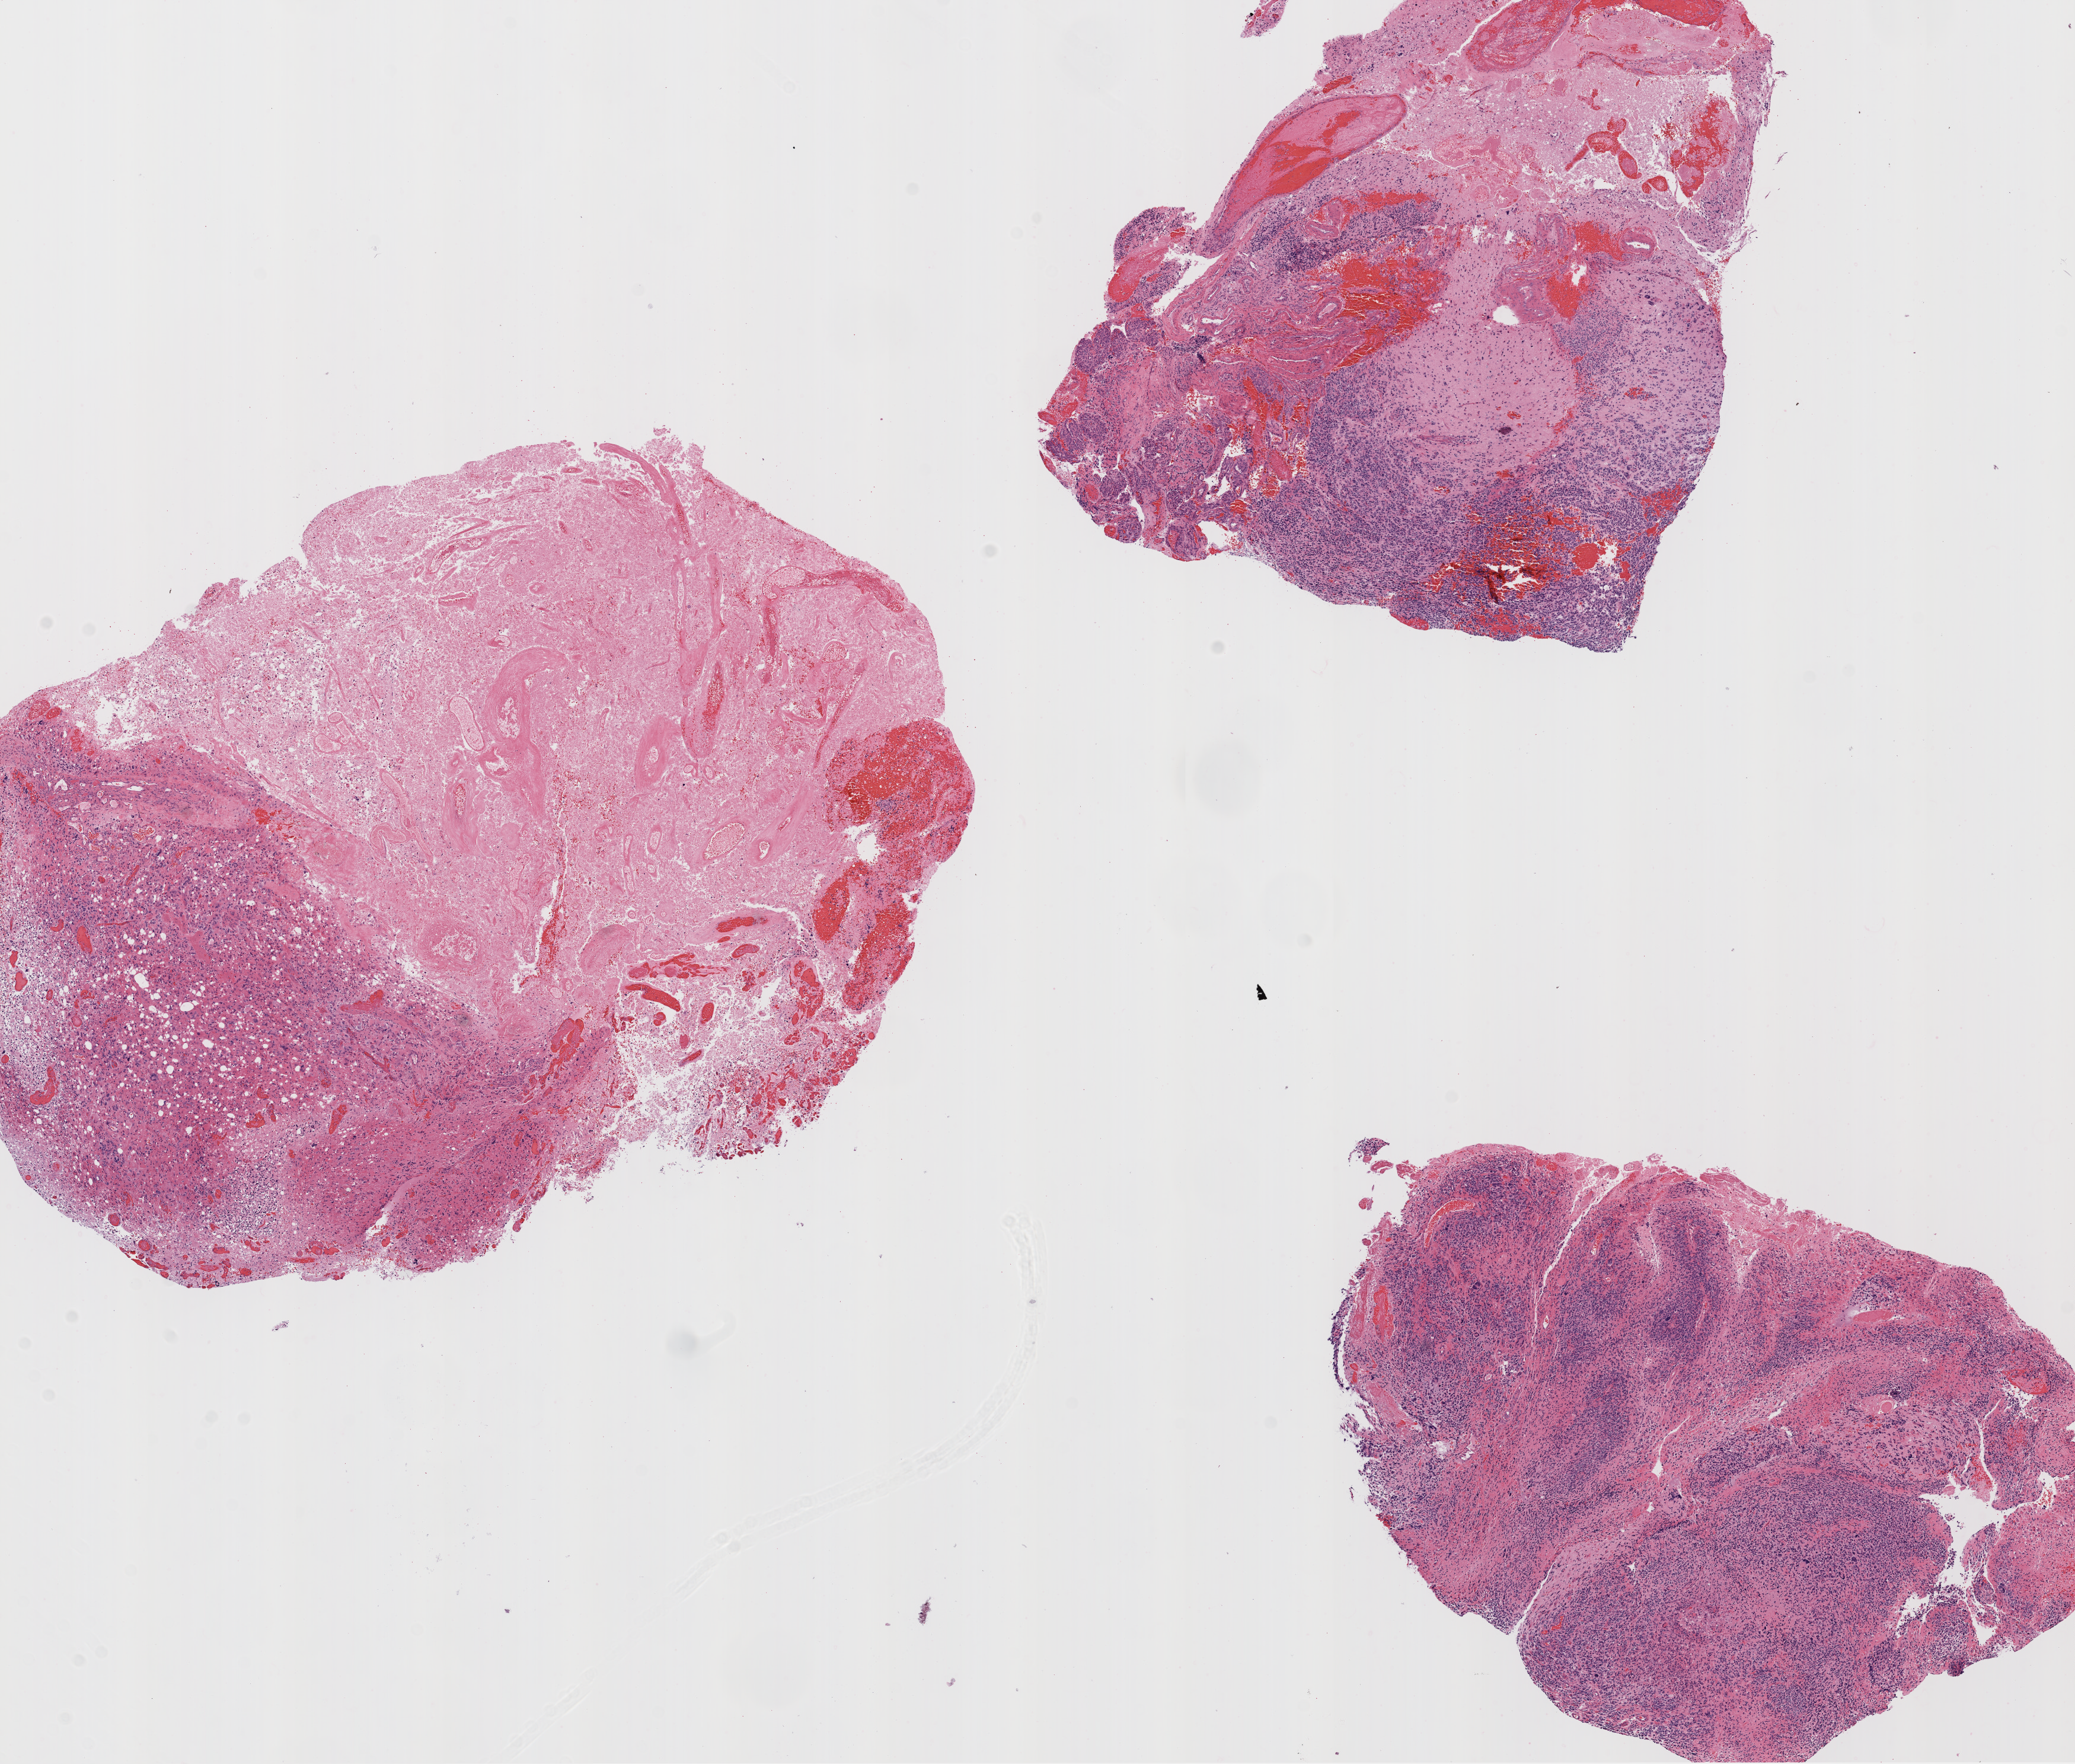
H&E-stained whole-slide image — whole scanned area (about 14.0 x 11.9 mm, slide scanned at 20x) shown as a low-resolution overview; FFPE section; primary tumour sample from the brain. Female, age 72 years at initial diagnosis.
* pathologic diagnosis: Glioblastoma